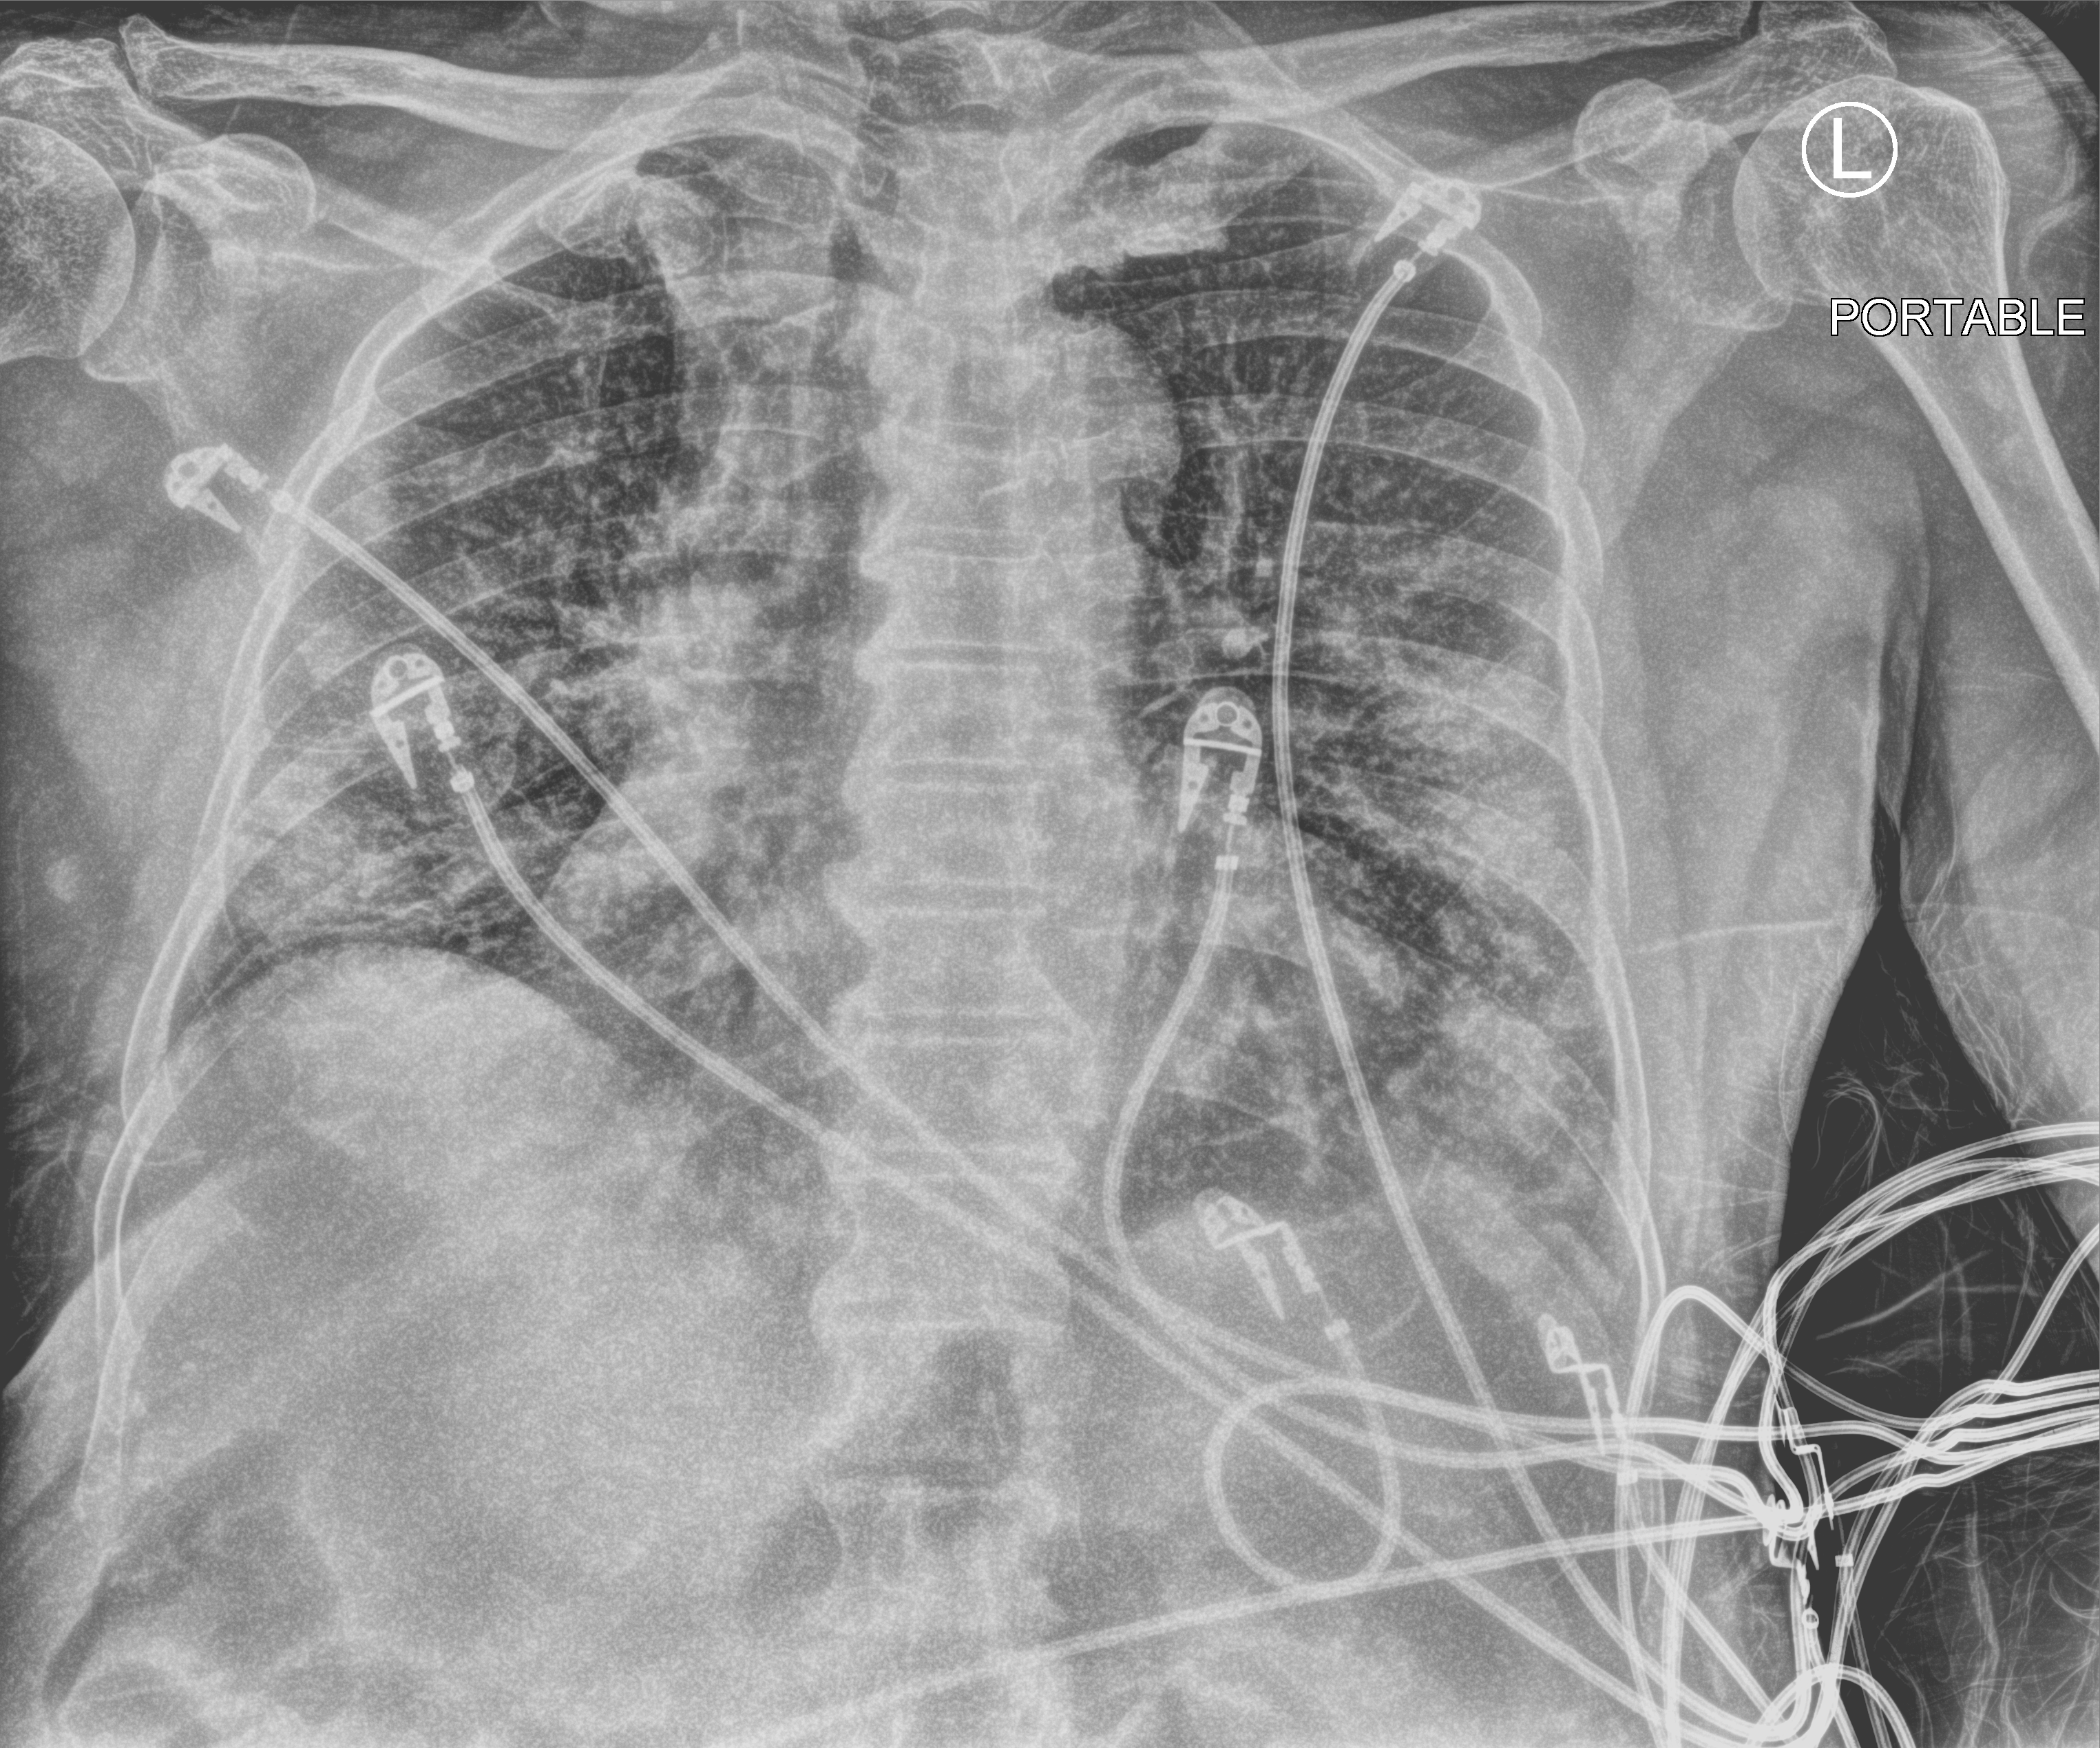
Chest X-ray (portable). Patient hospitalised with COVID-19; male, aged 60–74 years.
From the hospital-stay record, not from the radiograph (when in the stay this image was taken is not recorded): admitted to intensive care during this hospital stay: yes; chronic kidney disease (admission record): no; length of hospital stay: 26 days.